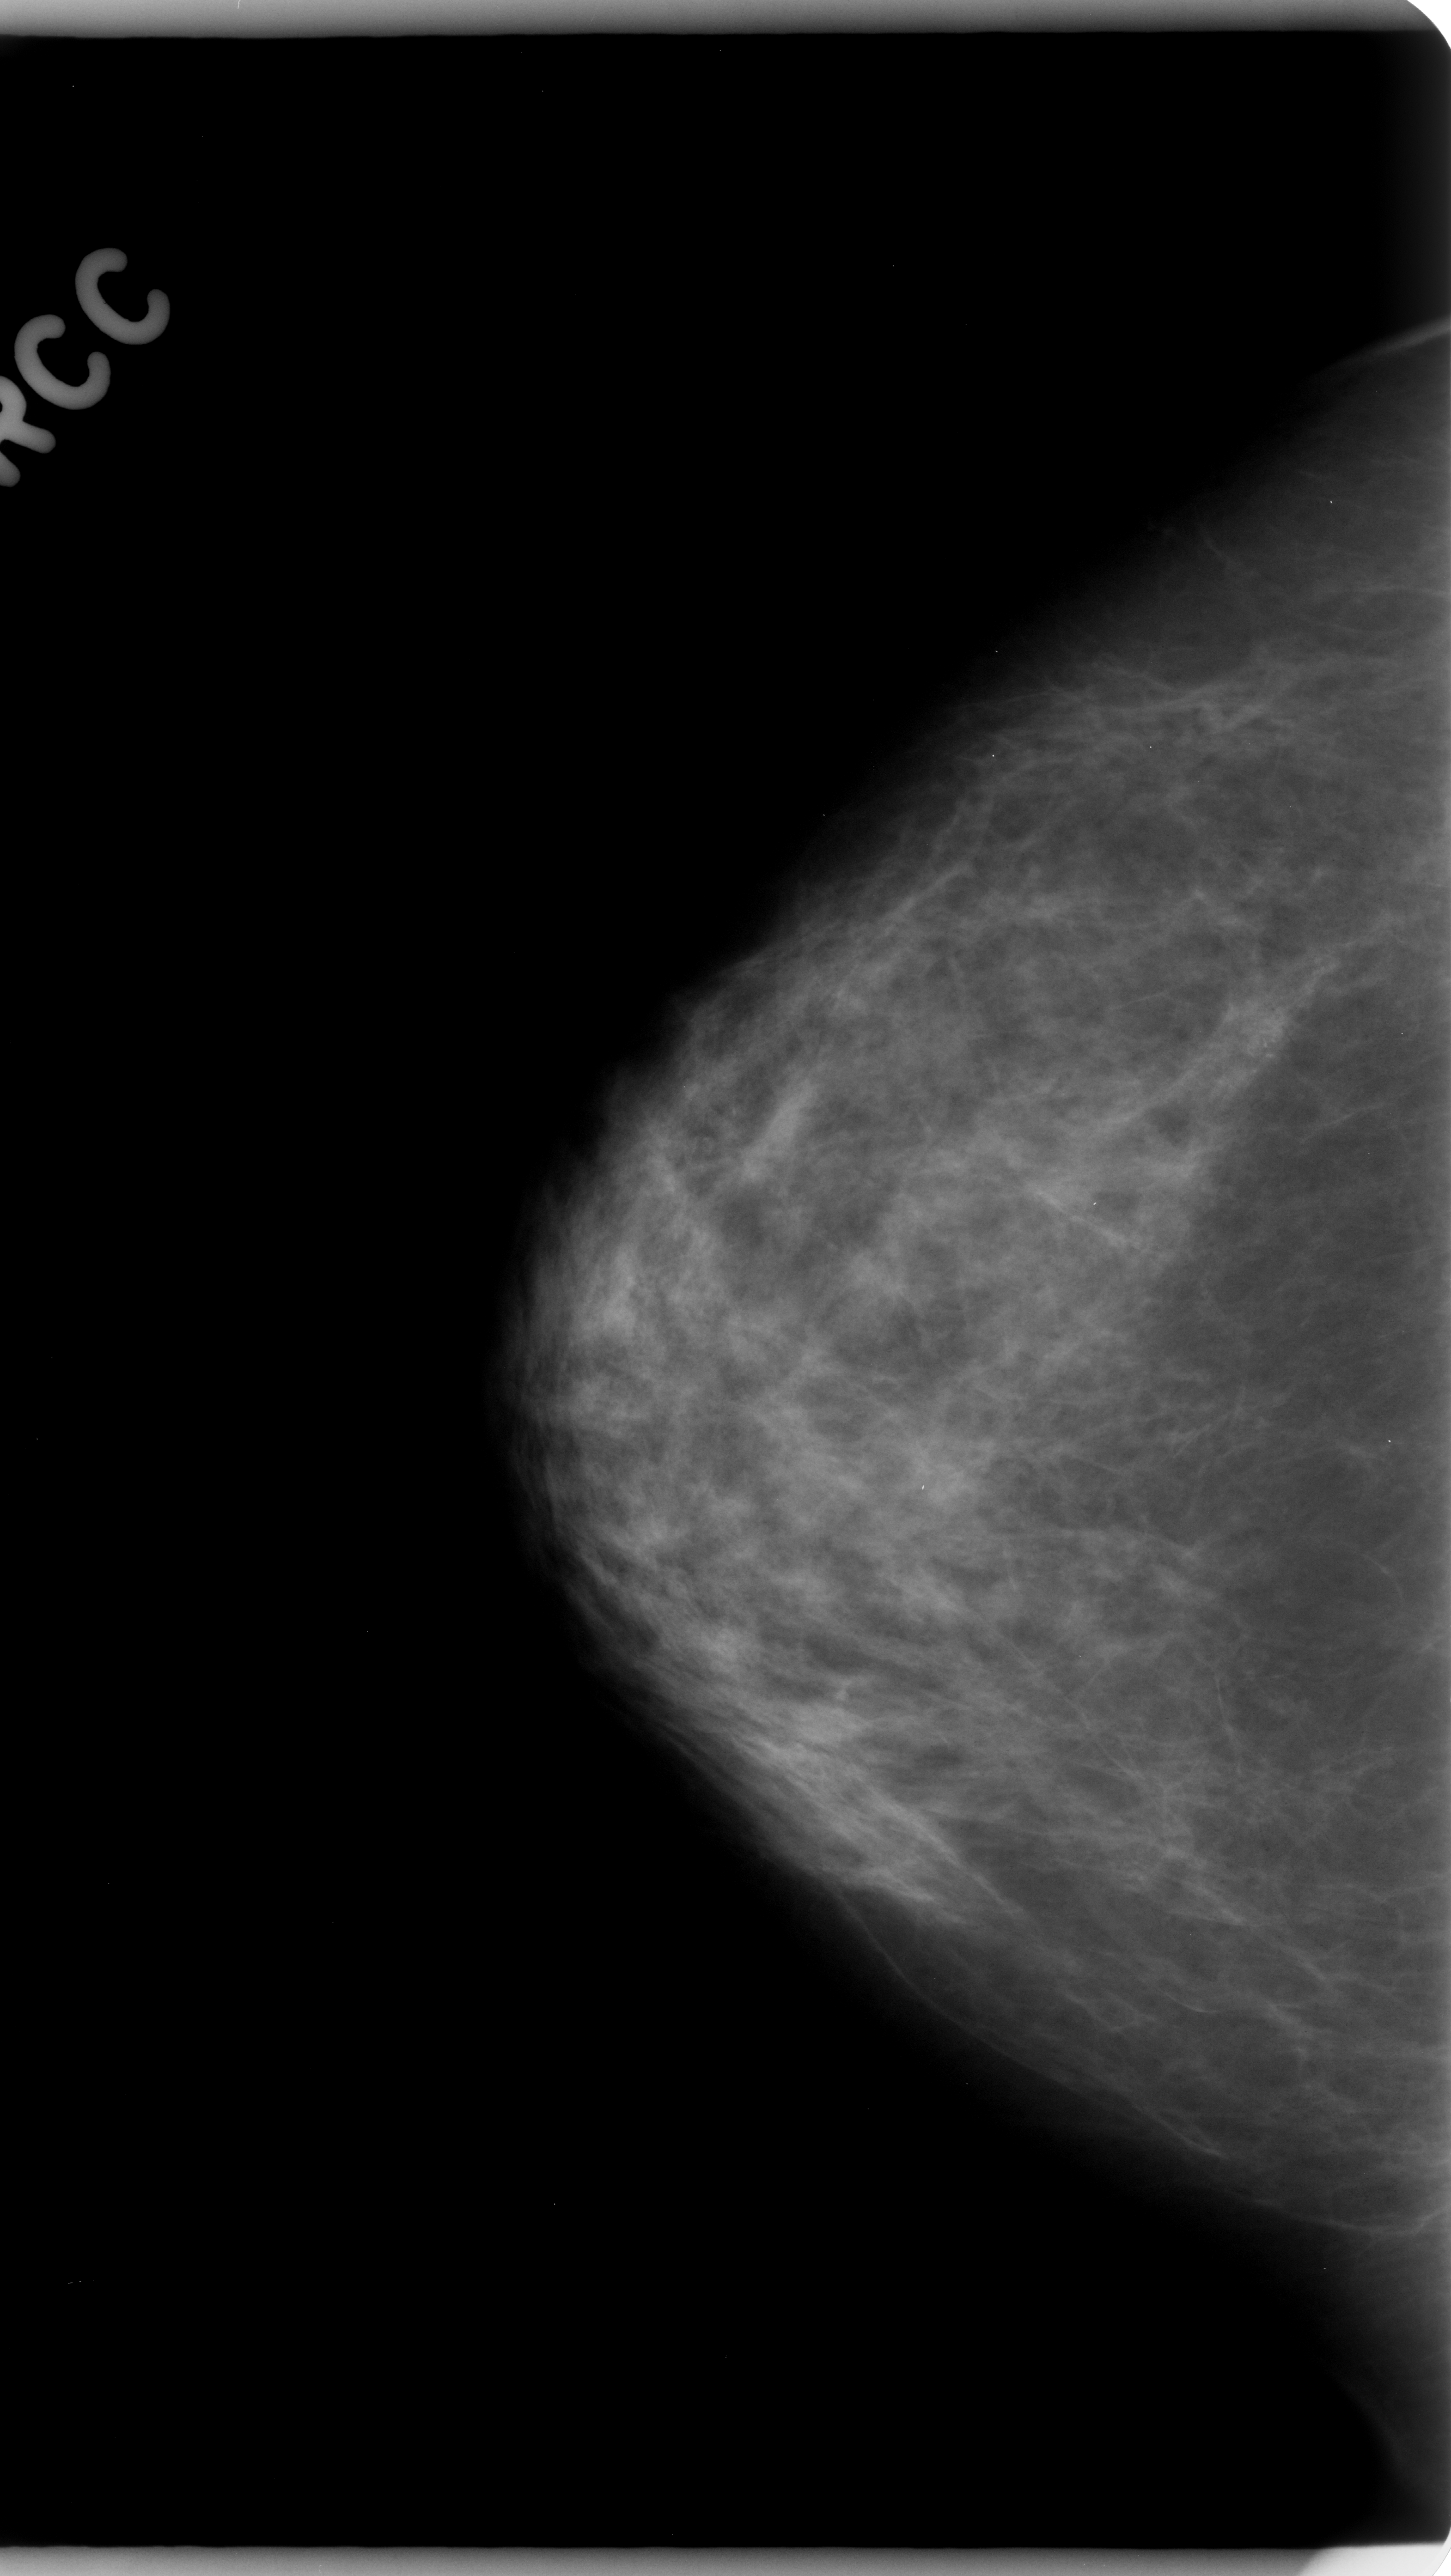
Scanned film-screen mammogram. Right breast. Craniocaudal (CC) view. BI-RADS breast density category 2 (scale 1–4). 1451 × 2576 image matrix.
Expert-marked regions of interest on this image (one box per marked abnormality):
- calcifications, morphology pleomorphic, distribution clustered; BI-RADS assessment category 4; pathology (as recorded): malignant: box from (x=1180, y=915) to (x=1395, y=1139) px